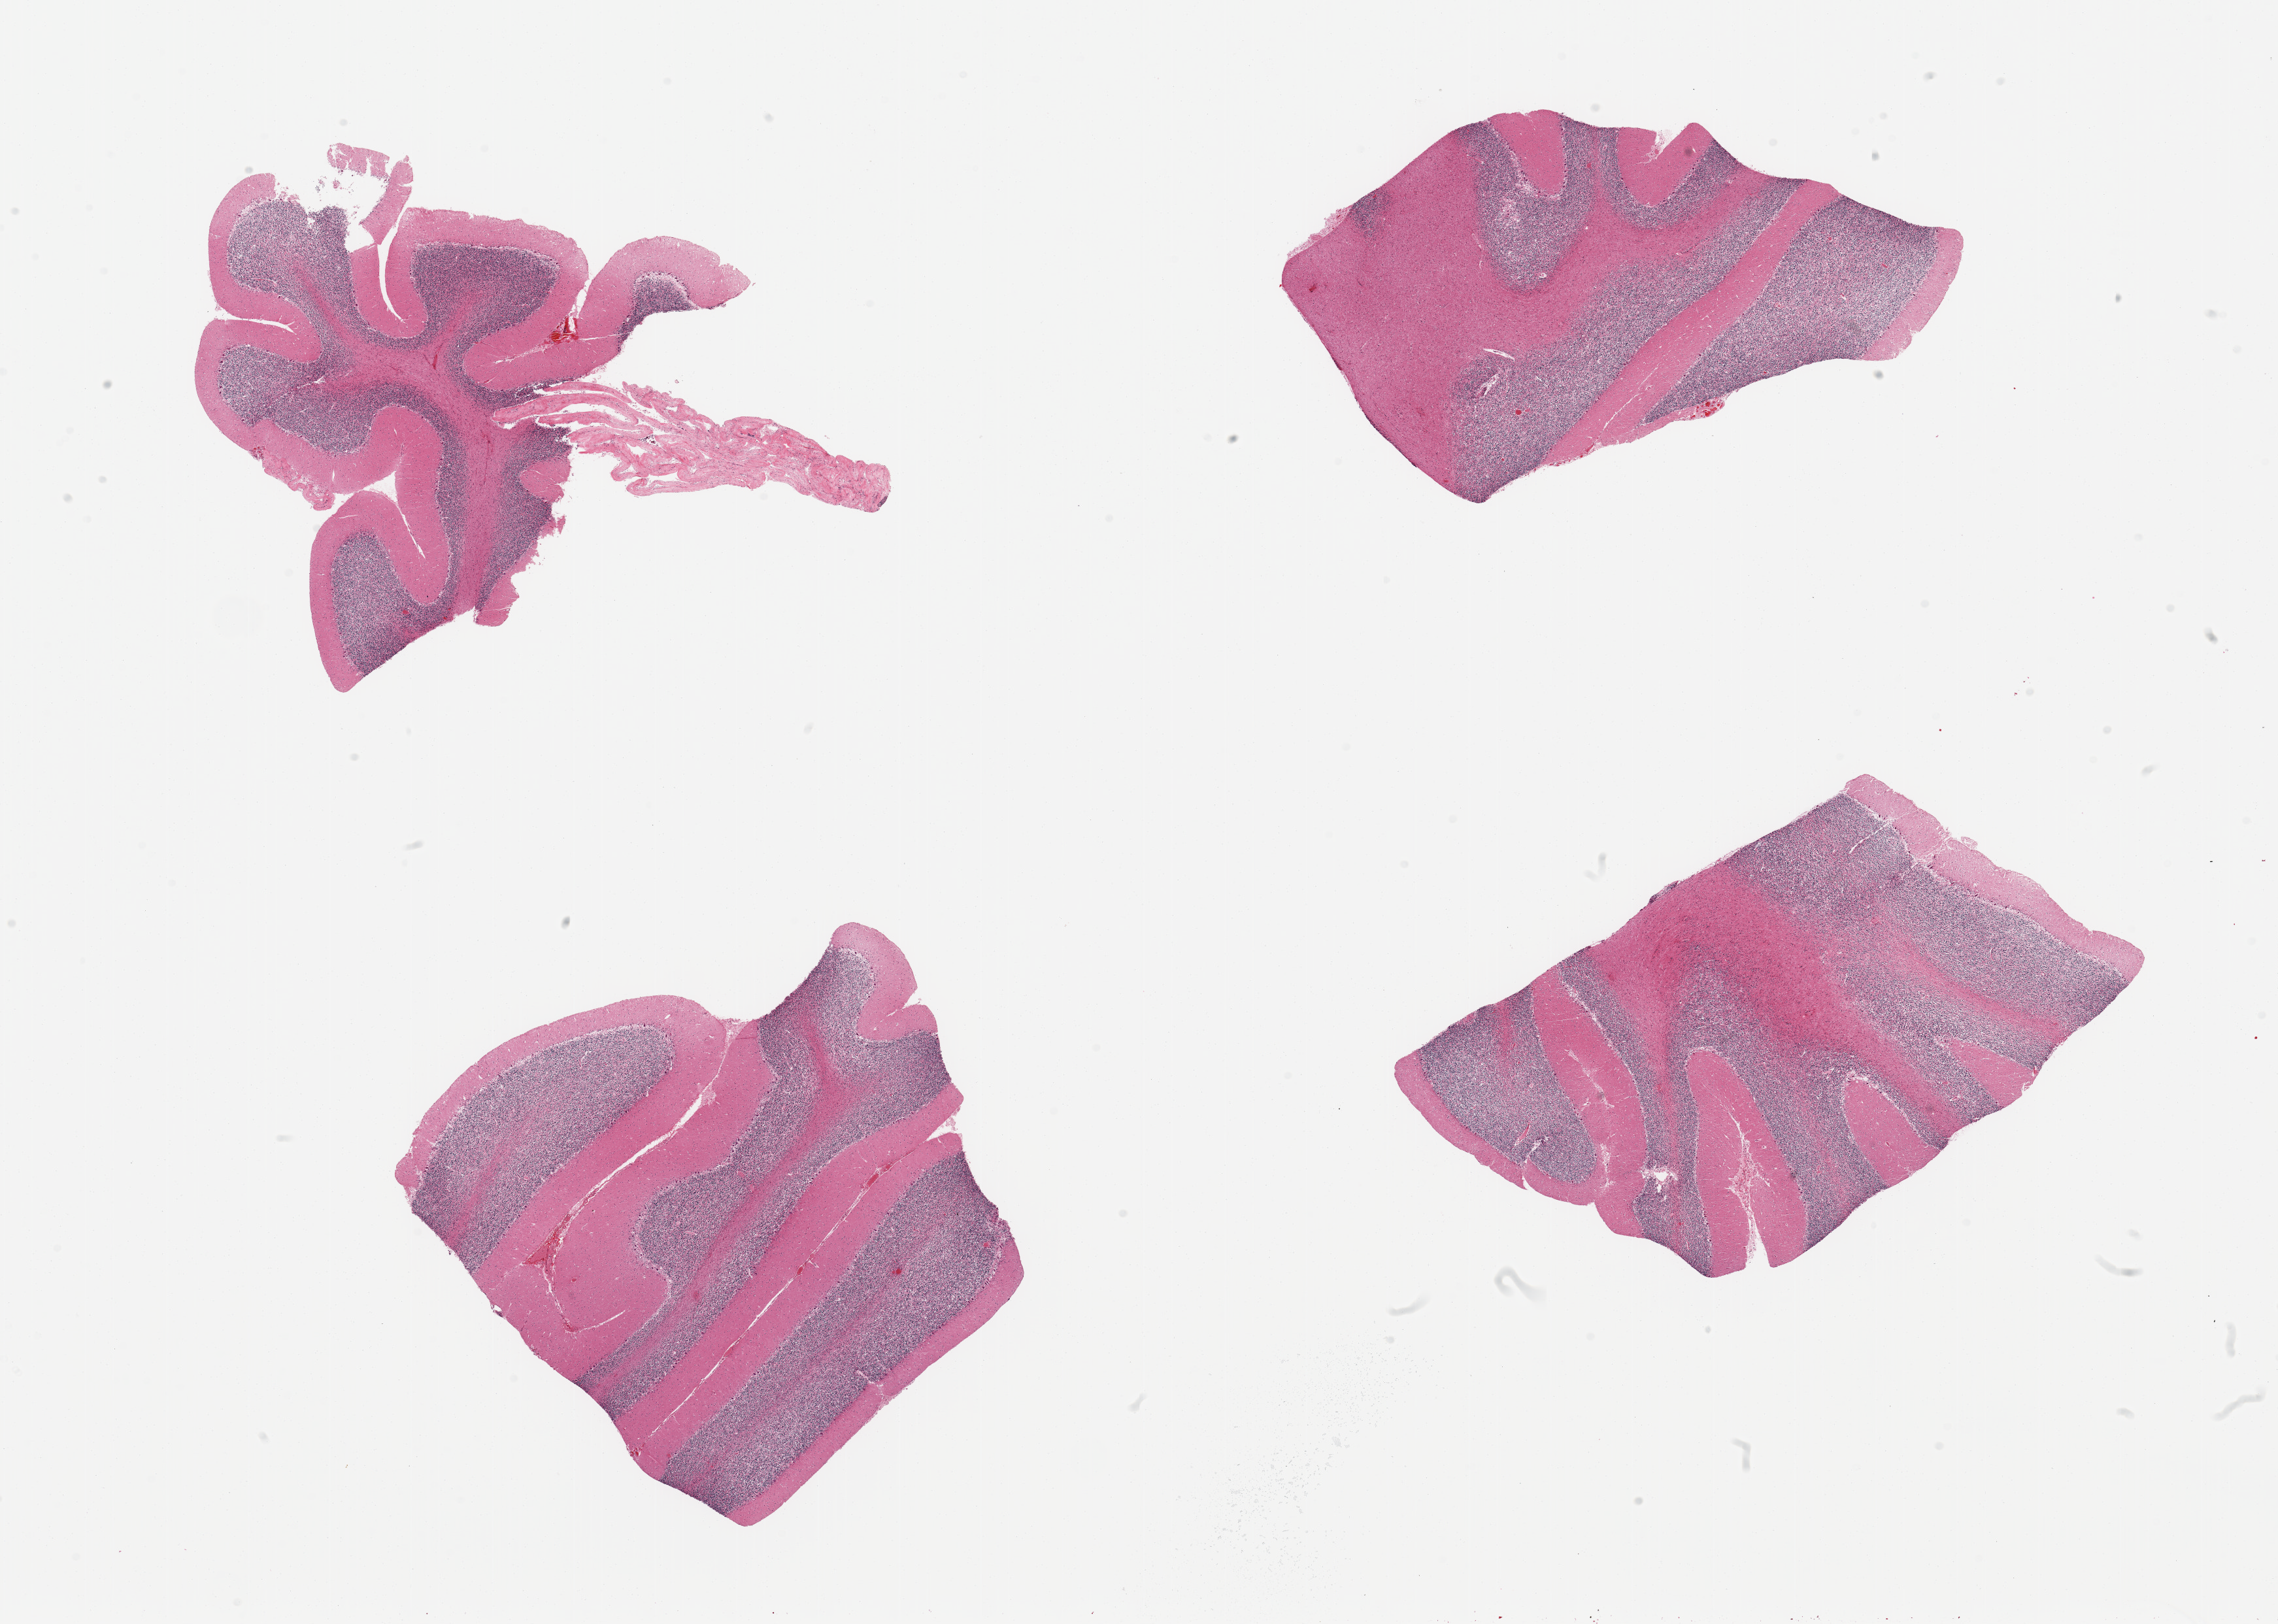
Digitized H&E-stained section, low-resolution overview of the scanned area, about 27.6 x 19.7 mm. PAXgene-fixed paraffin-embedded (PFPE) section. Sampled site (target tissue): cerebellum. Tissue donor sample. Donor: male.
Reviewer comment on this tissue sample: 4 pieces; mild to moderate autolysis.